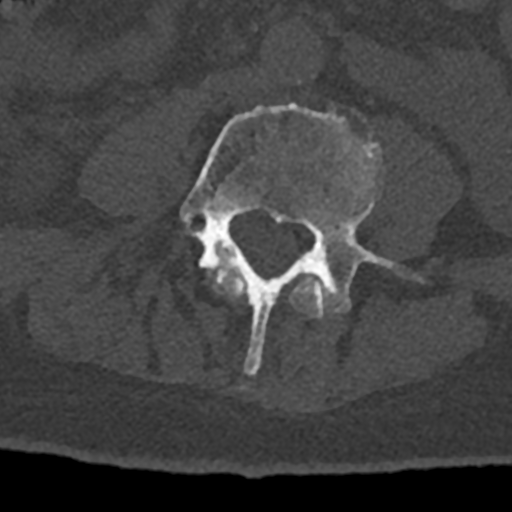
CT including the spine, one axial slice. Position 267 of 797 along the scan axis. Reconstruction kernel Br40s/3. 120 kVp. Bone window (W 1800 / L 400 HU). 0.5 mm slice thickness. 512 × 512 image matrix, field of view 160 × 160 mm. Male patient, age 74 years. Case-level facts recorded for this patient, not image findings: primary cancer: renal.
Structures marked on this image (semi-automatic segmentation, software-assisted and operator-edited):
- L3 vertebra: box from (x=213, y=266) to (x=332, y=318) px
- L4 vertebra: (x=180, y=103)–(x=421, y=374)